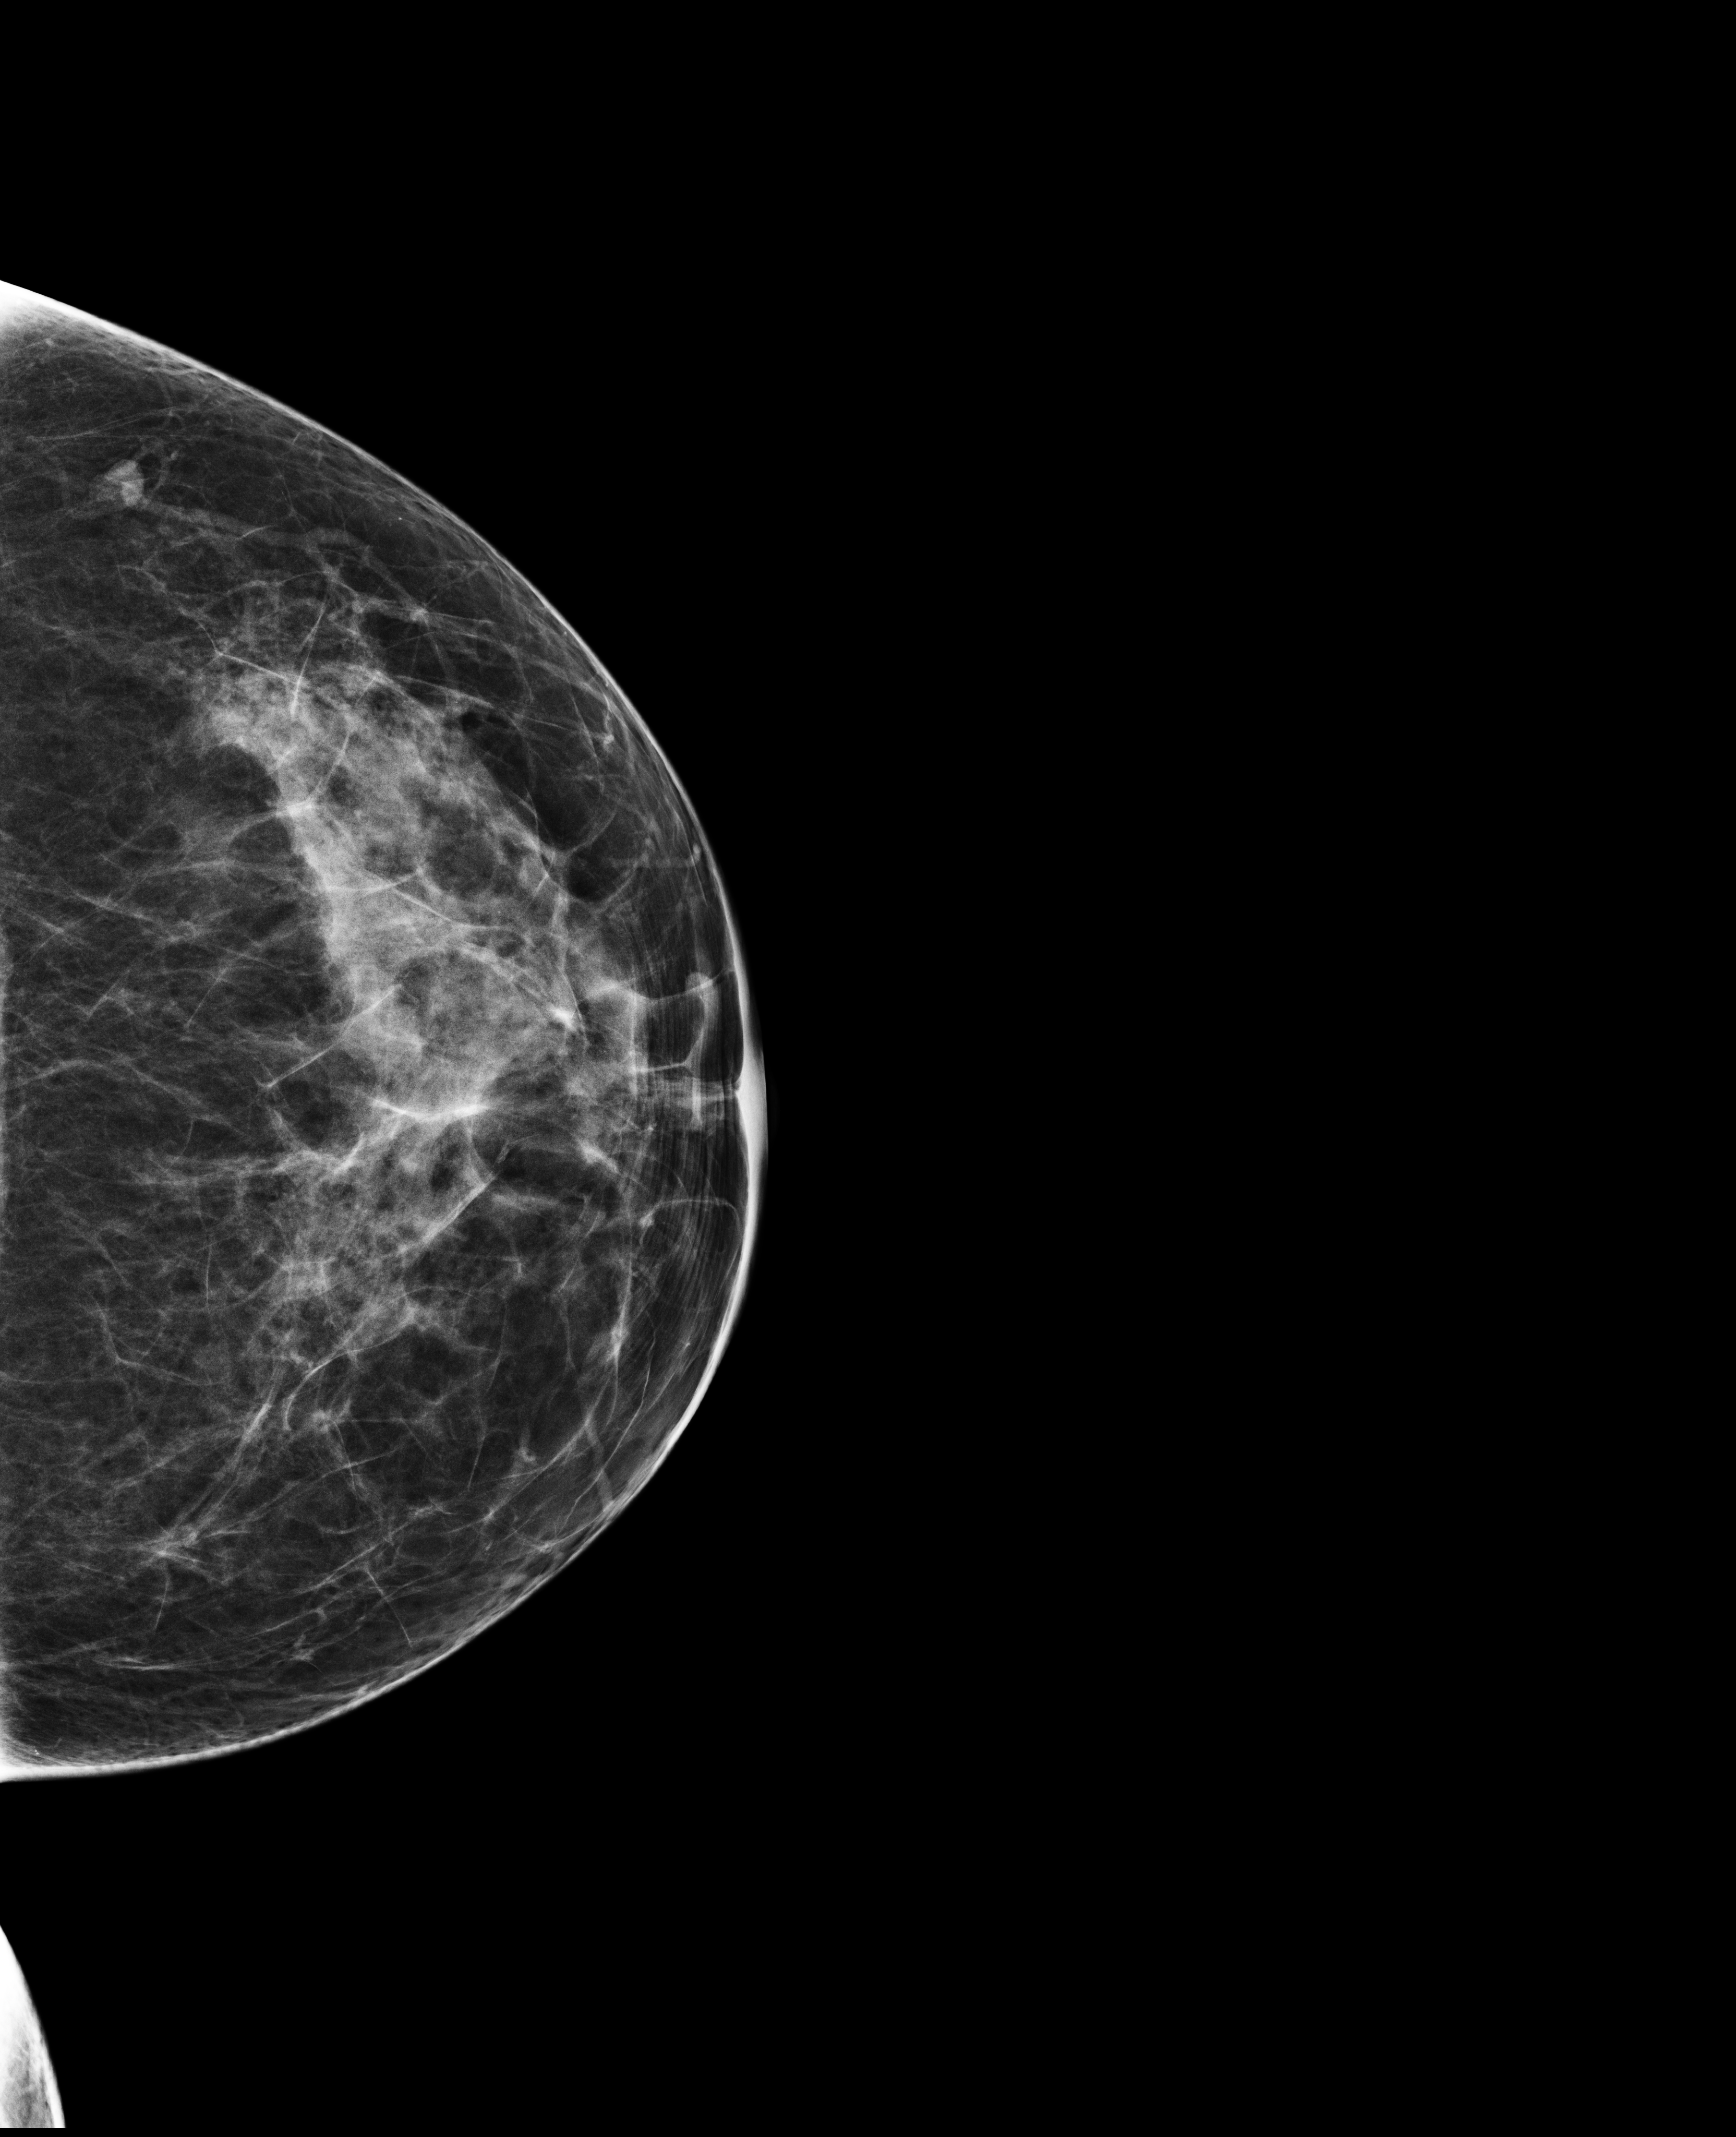
Annual screening mammography examination; compressed breast thickness 60 mm; system: Selenia Dimensions. Patient: female, 43 years.
Image type: full-field digital mammogram. Breast: left. Projection: craniocaudal (CC) view.